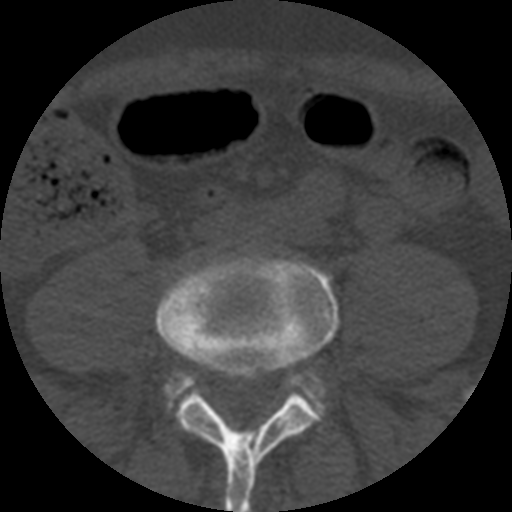
CT including the spine, one axial slice. Position 82 of 508 along the scan axis. Bone window (W 1800 / L 400 HU). 1.25 mm slice thickness. 512 × 512 image matrix. Patient age 57 years. Case-level facts recorded for this patient, not image findings: primary cancer: prostate.
Annotated regions visible in this slice (semi-automatically segmented with operator editing):
- L4 vertebra: bounding box [x1, y1, x2, y2] px = [155, 253, 339, 512]
- L5 vertebra: [166, 372, 324, 415]